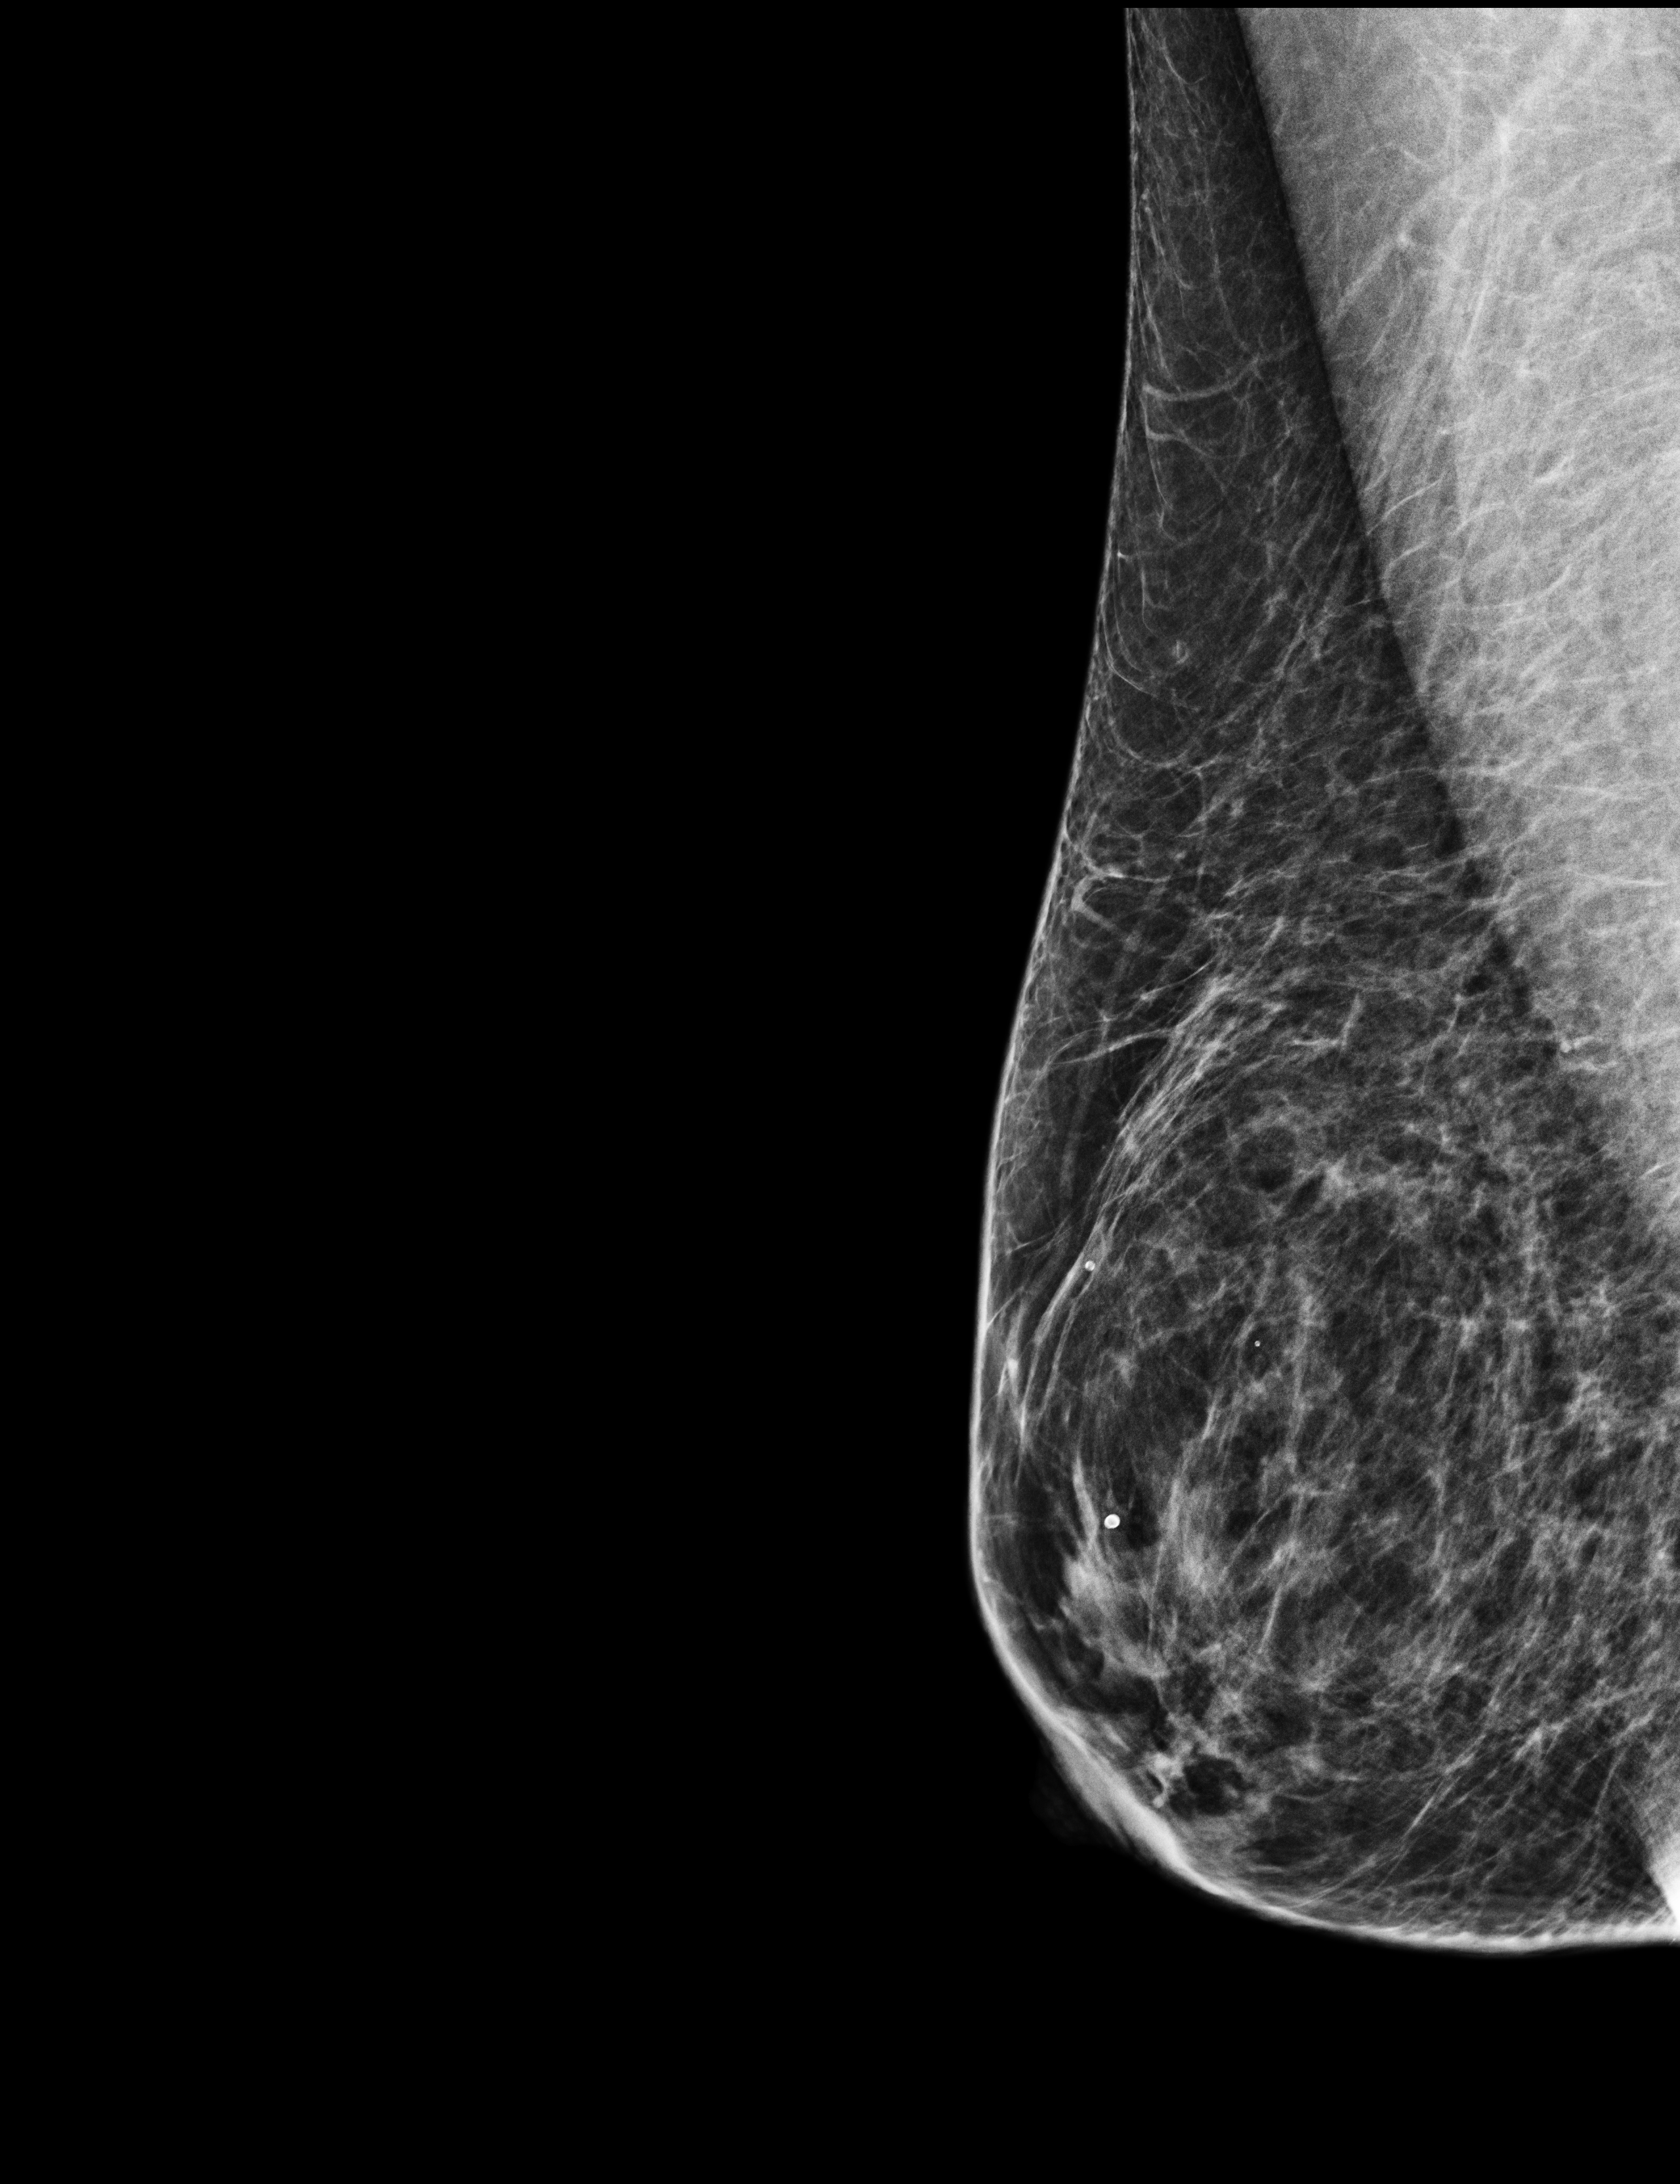
Annual screening mammography examination; compressed breast thickness 52 mm. Patient aged 52 years (female).
Image type: full-field digital mammogram. Breast: right. Projection: MLO view.